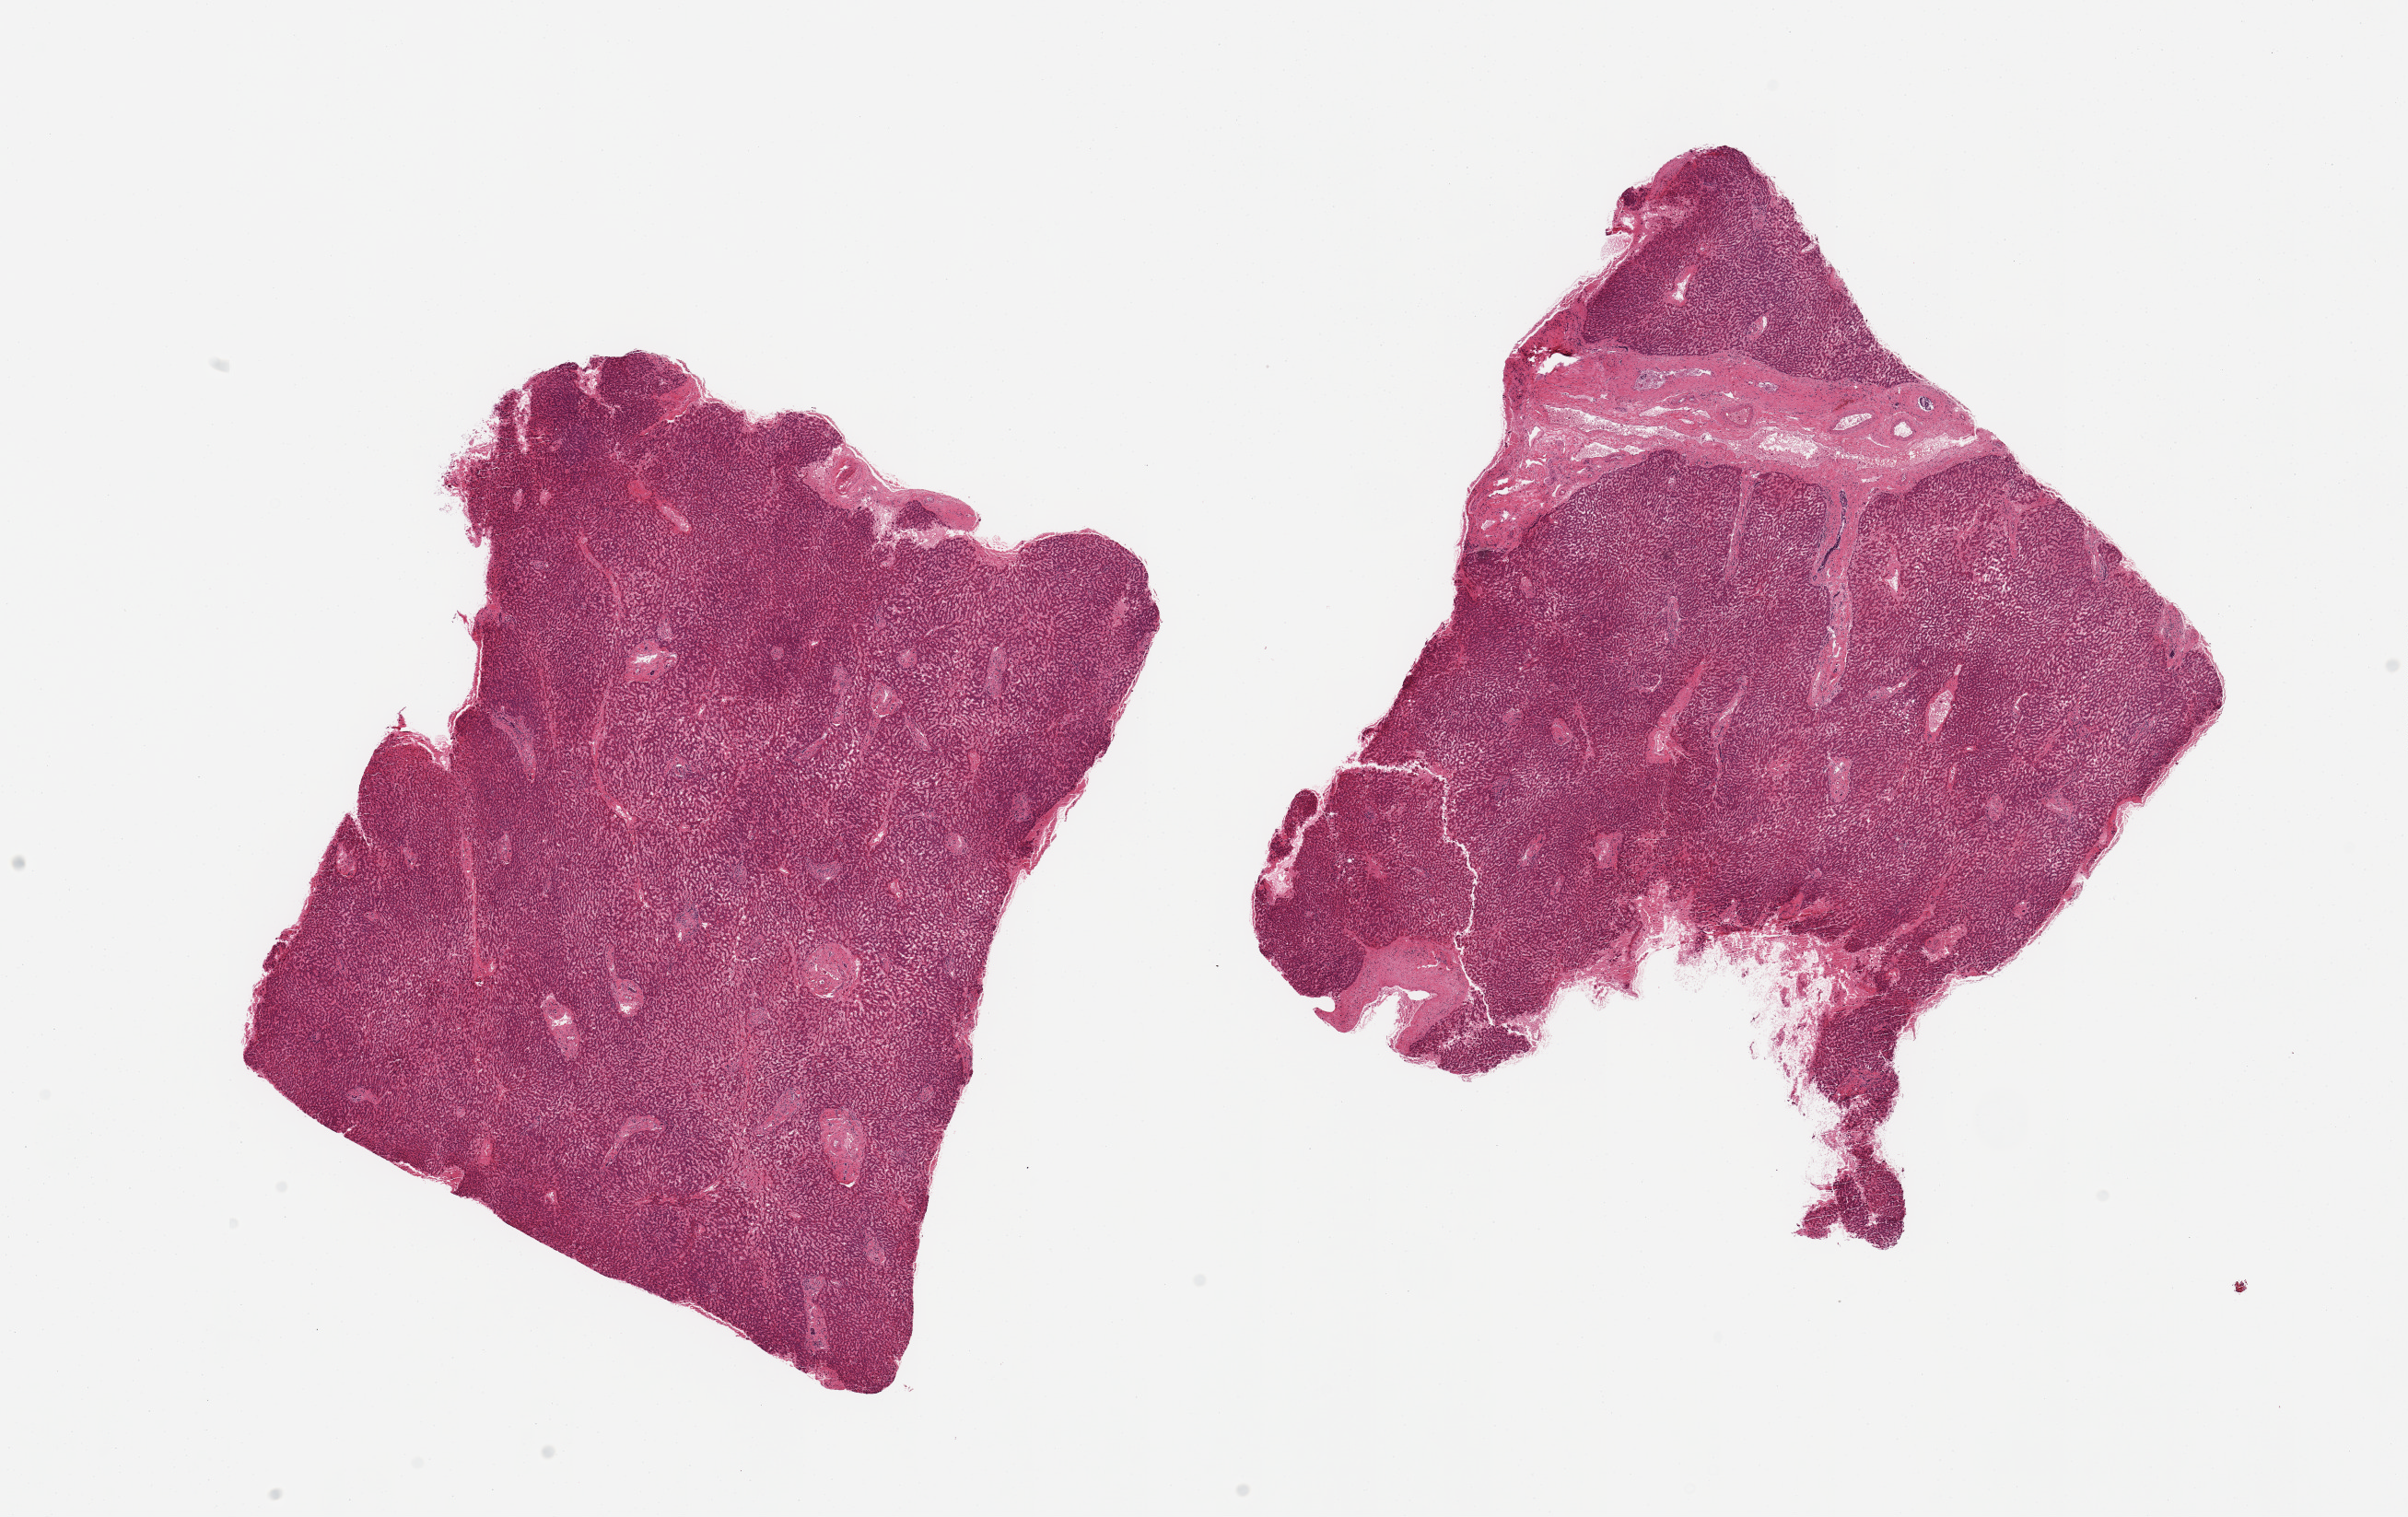
Digitized H&E-stained section — a low-resolution overview of the entire scanned area, about 20.7 x 13.0 mm (acquisition: 20x scan); PAXgene-fixed, paraffin-embedded tissue; target tissue: liver; donor tissue sample. Donor: female.
• reviewer comment on this tissue sample: 2 pieces; grade 1 to 2 autolysis; passive congestion